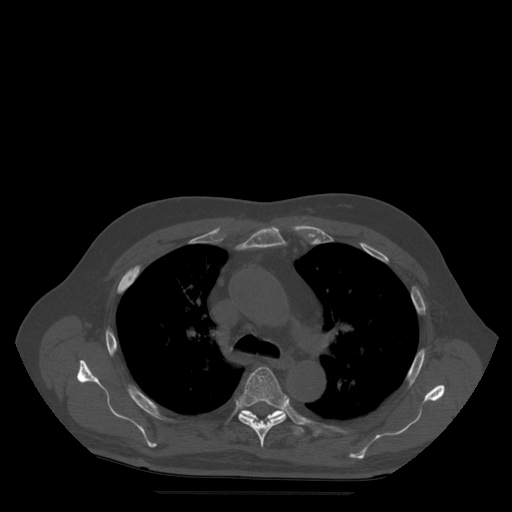
CT including the spine, one axial slice; position 368 of 522 along the scan axis; bone window (W 1800 / L 400 HU); 512 × 512 image matrix. Patient age 72 years. Case-level facts recorded for this patient, not image findings: primary cancer: prostate.
Structures marked on this image (semi-automatically segmented with operator editing):
- T5 vertebra: box from (x=236, y=368) to (x=289, y=448) px
- T6 vertebra: (x=243, y=410)–(x=304, y=435)